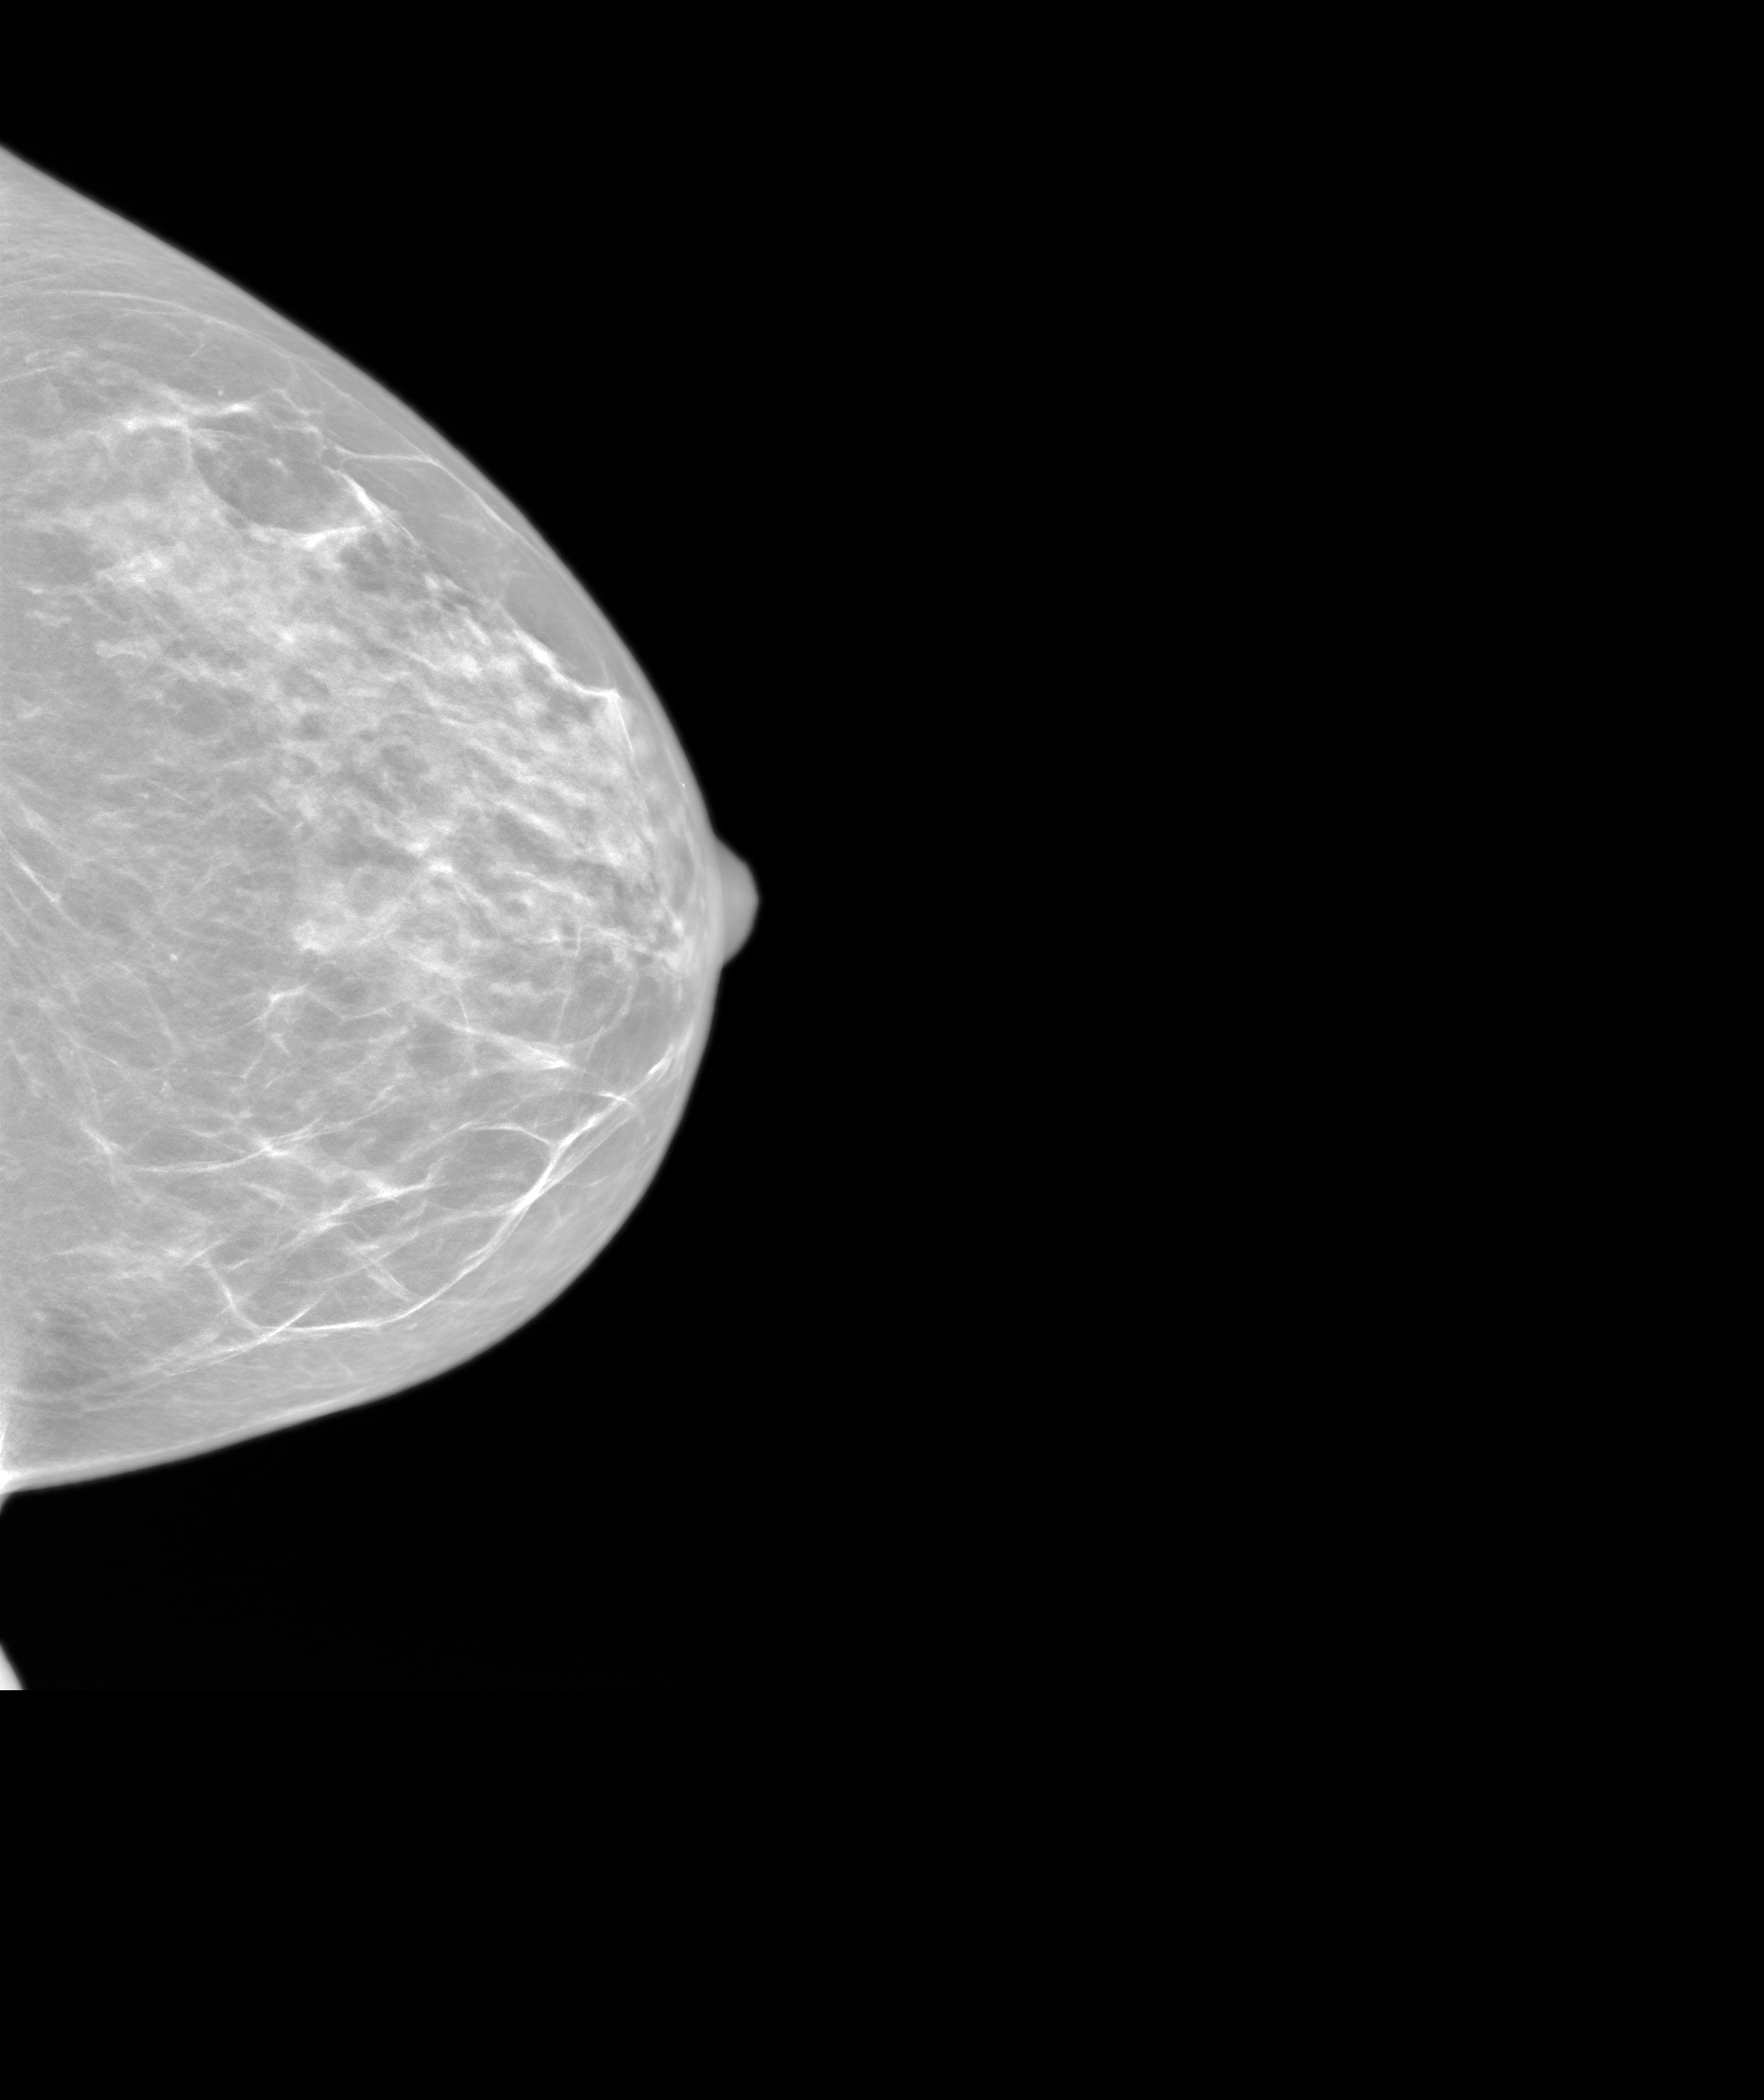
Screening examination. Patient aged 57 years (female).
Image type: synthesized 2-D view from tomosynthesis. Breast: left. Projection: CC view.